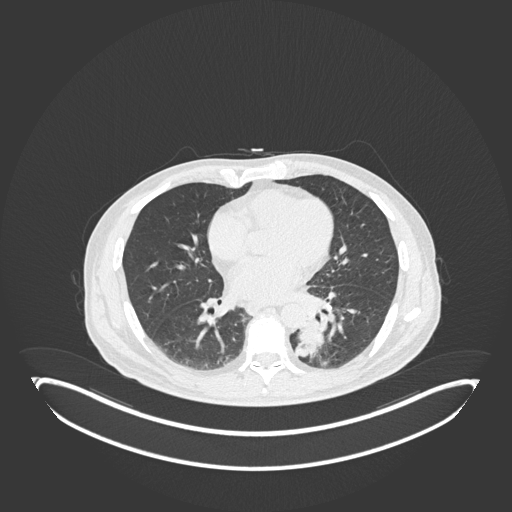
Chest CT, one axial slice. Position 74 of 251 along the scan axis. 120 kVp. Lung window (W 1500 / L -600 HU). 1 mm slice thickness. 512 × 512 image matrix, field of view 500 × 500 mm. Male patient, age 72 years. Case-level facts recorded for this patient, not image findings: clinical TNM (as recorded): T2b N0 M1.
Outlined on this slice (bounding box drawn by a radiologist):
- lung tumour (recorded histology: adenocarcinoma): bounding box <298,318,327,360> (left, top, right, bottom; pixels)